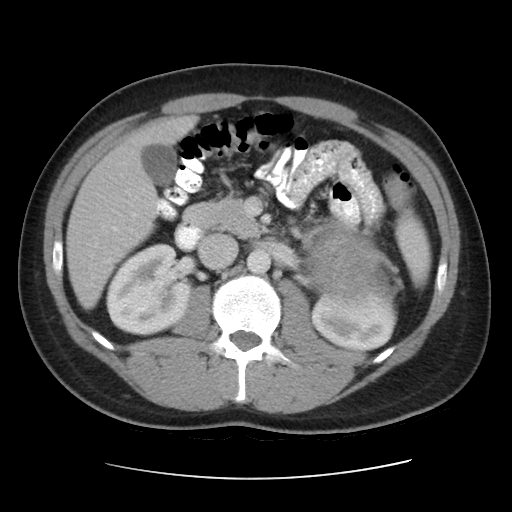
Contrast-enhanced abdominal CT, one axial slice; slice 21 of 48 in the series (ordered by position); 120 kVp; intravenous contrast given; soft-tissue window (W 400 / L 40 HU); 512 × 512 image matrix, field of view 360 × 360 mm. Male patient, age 32 years. Case-level facts recorded for this patient, not image findings: diagnosis: adrenocortical carcinoma; tumour side: left adrenal; tumour size at pathology: 14 cm; Ki-67 index: 67 %; stage (as recorded): 3.
Annotated regions visible in this slice (semi-automatic segmentation, software-assisted and operator-edited):
- mass: bounding box <308,222,391,298> (left, top, right, bottom; pixels)